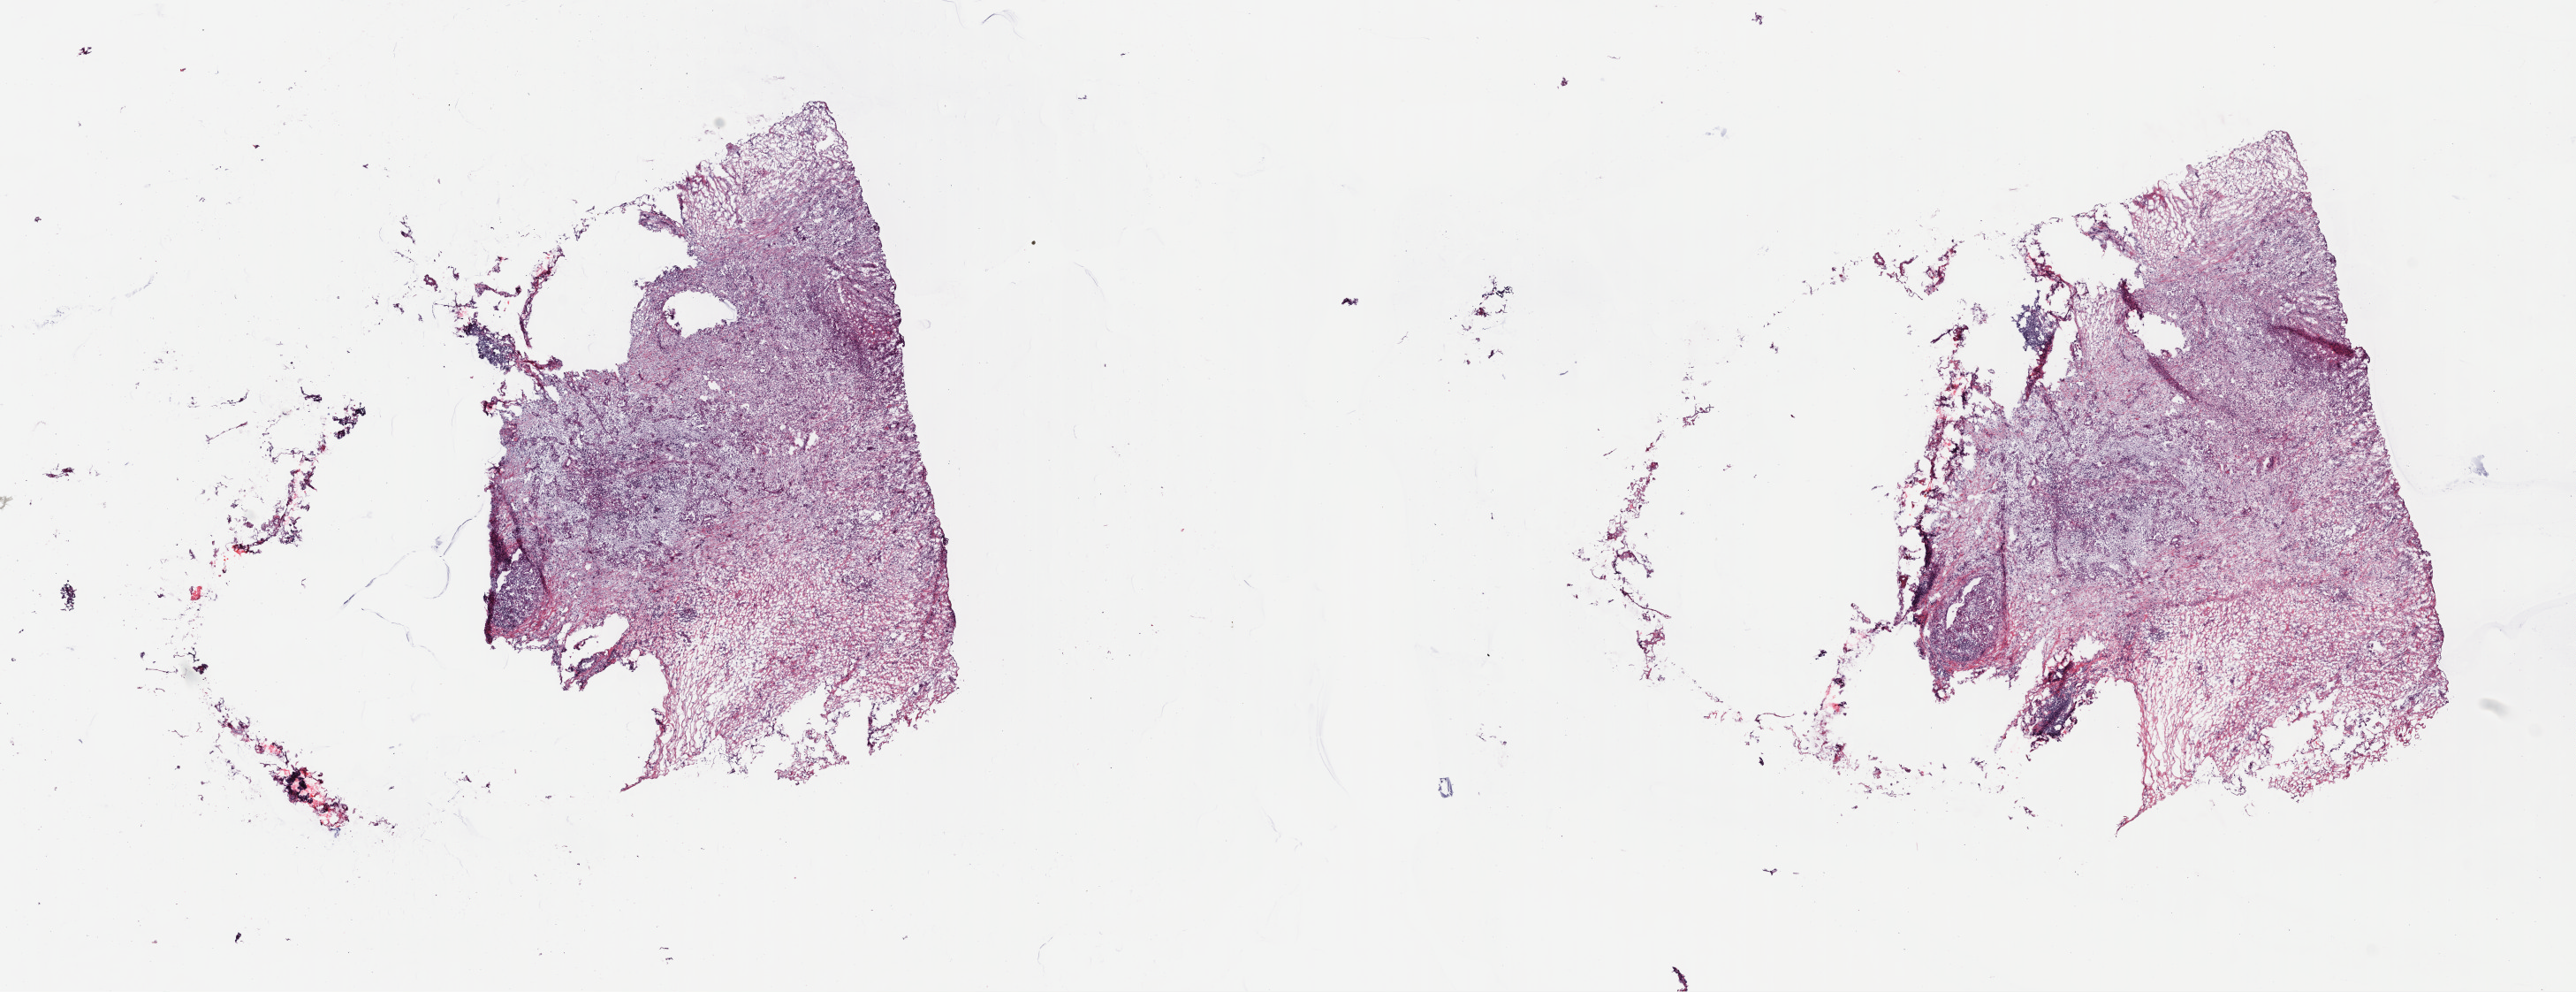
Digitized Hematoxylin and eosin (H&E) stained tissue section (whole slide) — whole scanned area (about 22.9 x 8.8 mm) shown as a low-resolution overview. Frozen section from the top of the tissue portion. Sample: primary tumour, pancreas. Male patient; age at initial diagnosis 58 years. Histologic grade: G2 (moderately differentiated). Slide review estimates, as recorded: tumour cells 50%, tumour nuclei 70%, normal cells 0%, stromal cells 50%, necrosis 0%. Infiltration values recorded for this section: lymphocyte infiltration 4%, monocyte infiltration 0%, neutrophil infiltration 0%.
AJCC pathologic stage: IIB (7th edition). Lymph nodes positive (case pathology): 4 of 18 examined. Diagnosis: Infiltrating duct carcinoma, NOS.